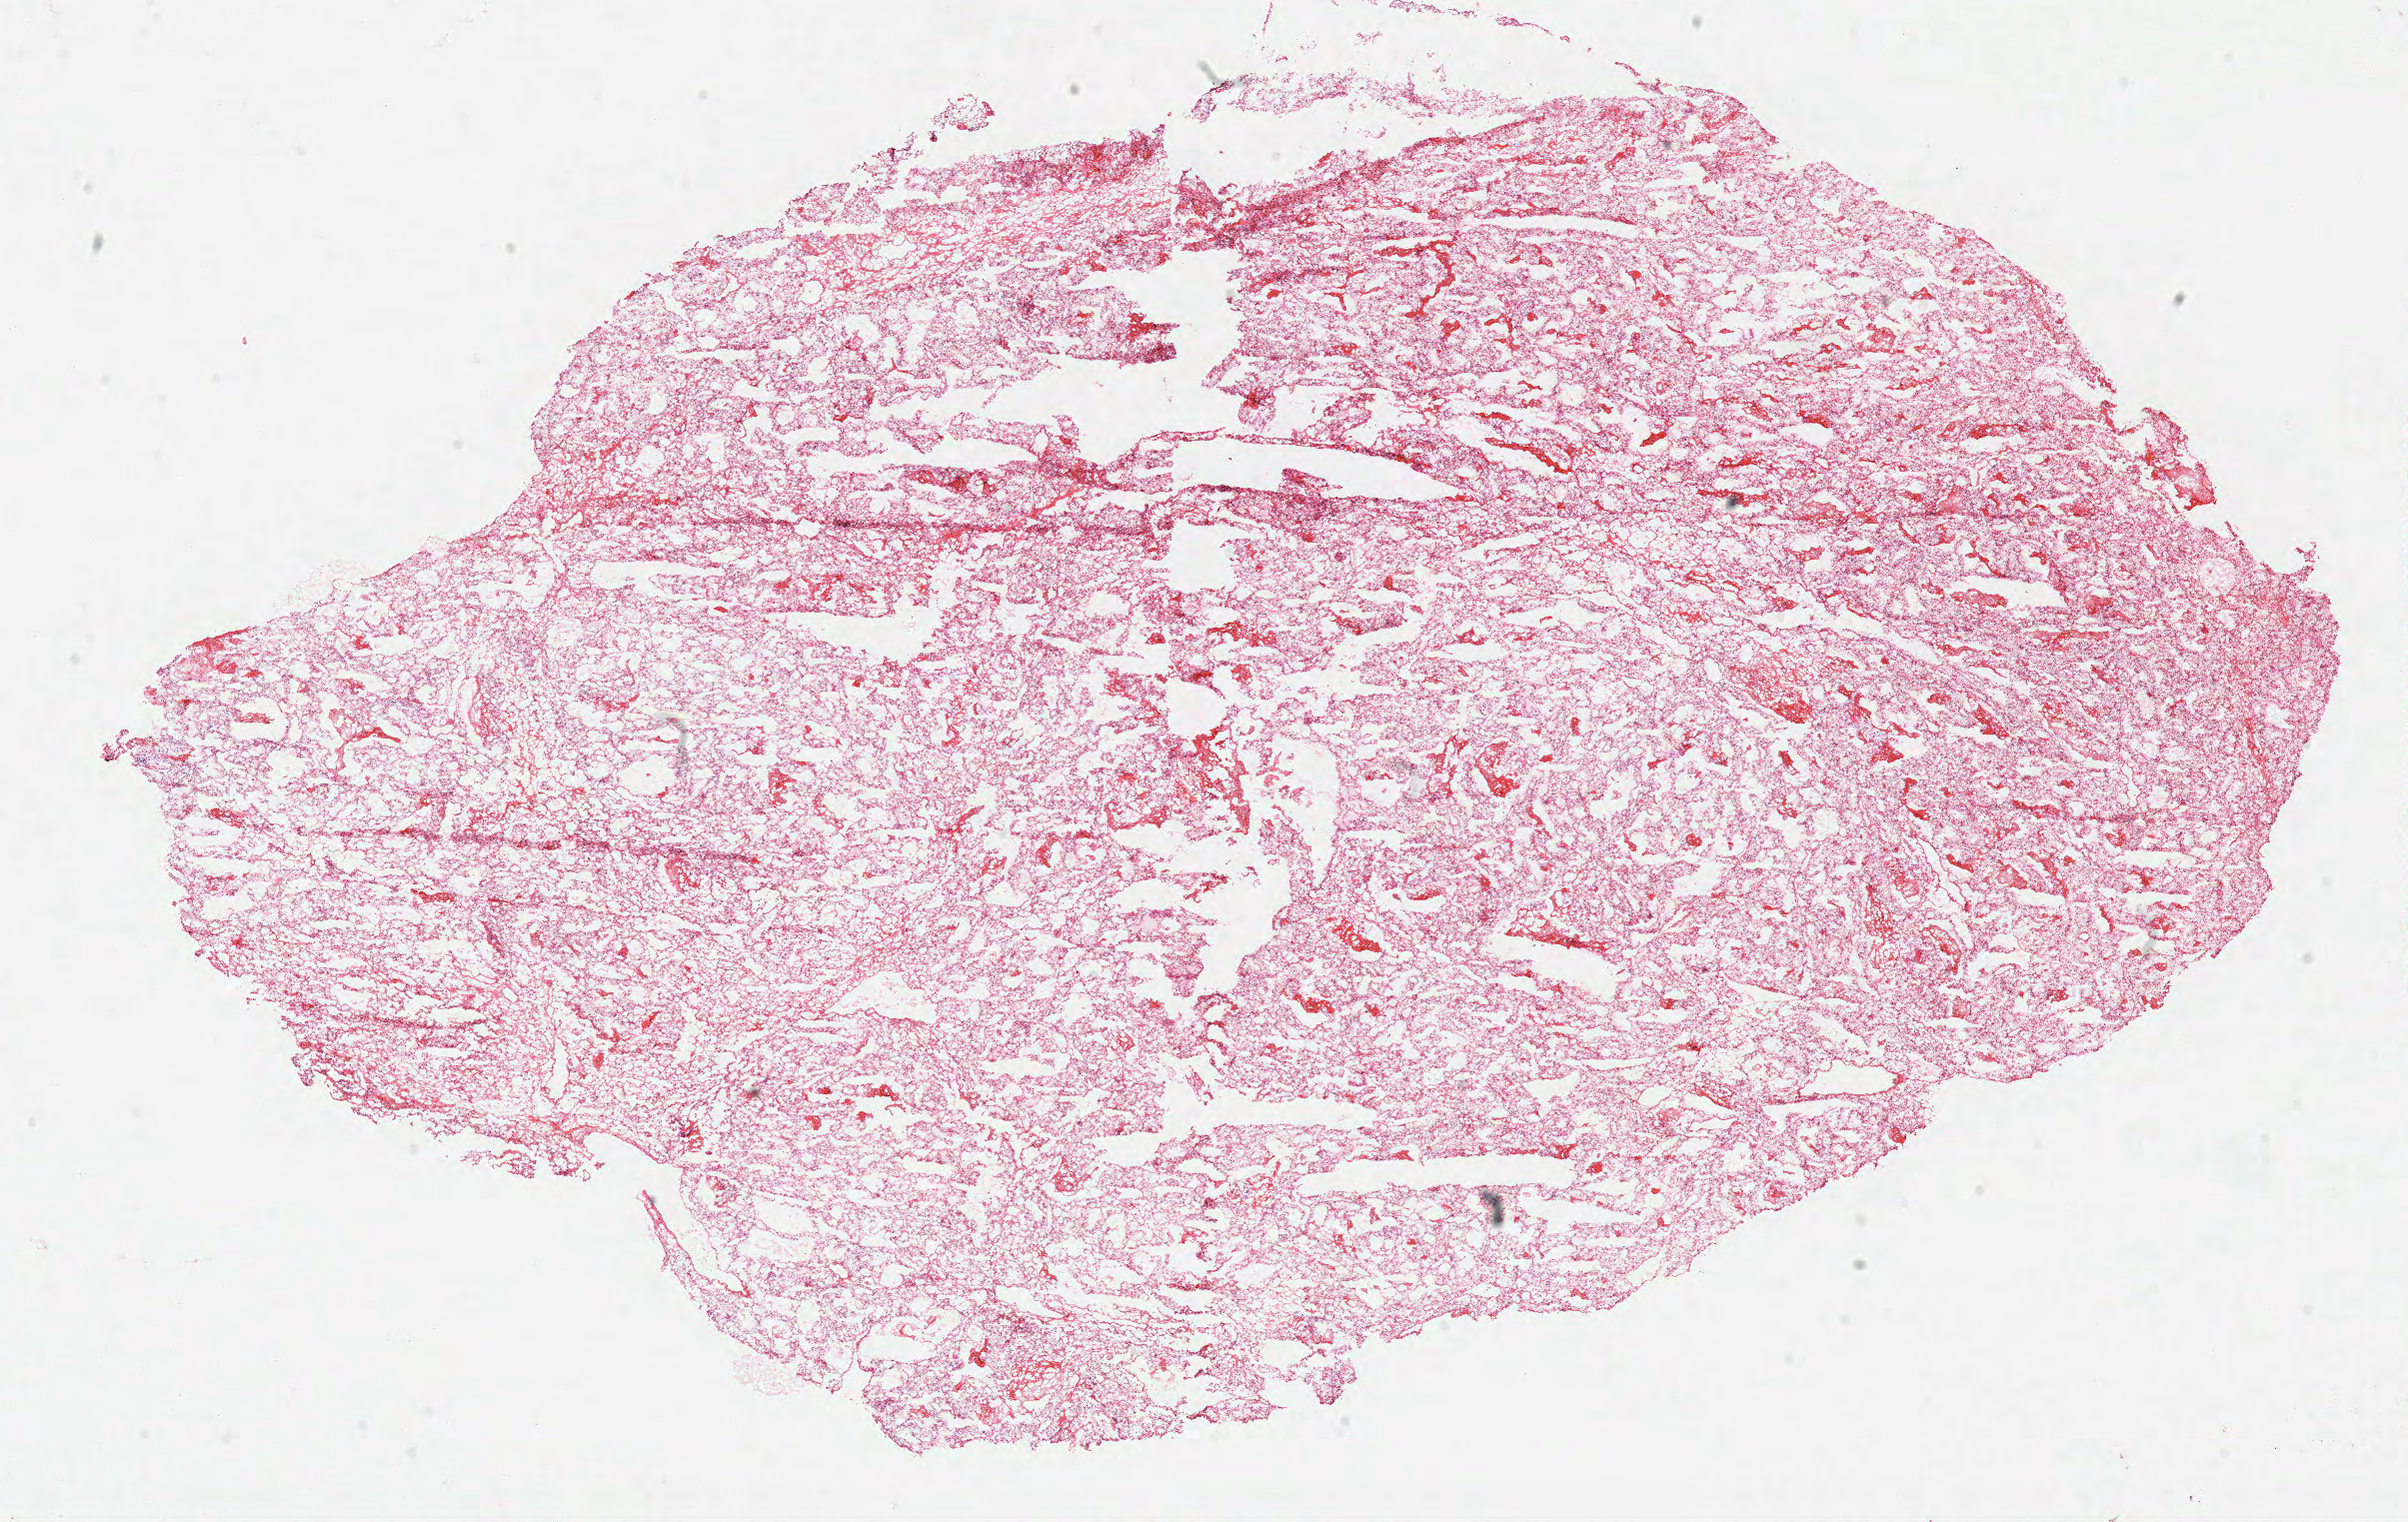
Whole-slide histology image, H&E — whole scanned area (about 19.0 x 12.0 mm, from a 40x scan) shown as a low-resolution overview, frozen section from the top of the tissue portion, primary tumour sample from the kidney. Male patient; age at initial diagnosis 38 years. Histologic grade: G2 (moderately differentiated). Composition of this section per pathologist review: tumour cells 90%, tumour nuclei 85%, normal cells 0%, stromal cells 10%, necrosis 0%.
- AJCC pathologic stage: I
- pathologic diagnosis: Clear cell adenocarcinoma, NOS